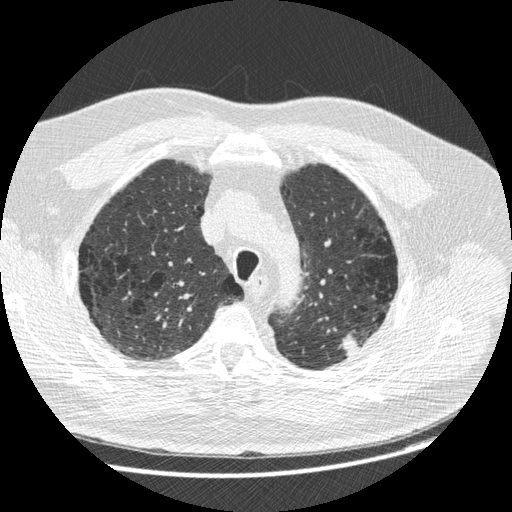
Low-dose screening chest CT, one axial slice; slice 206 of 258 in the series (ordered by position); reconstruction kernel STANDARD; lung window (W 1500 / L -600 HU); 1.25 mm slice thickness; 512 × 512 image matrix, field of view 370 × 370 mm.
Outlined on this slice (manually delineated by an expert):
- lesion 1 (tumor, upper lobe of left lung): bounding box [x1, y1, x2, y2] px = [341, 334, 359, 356]